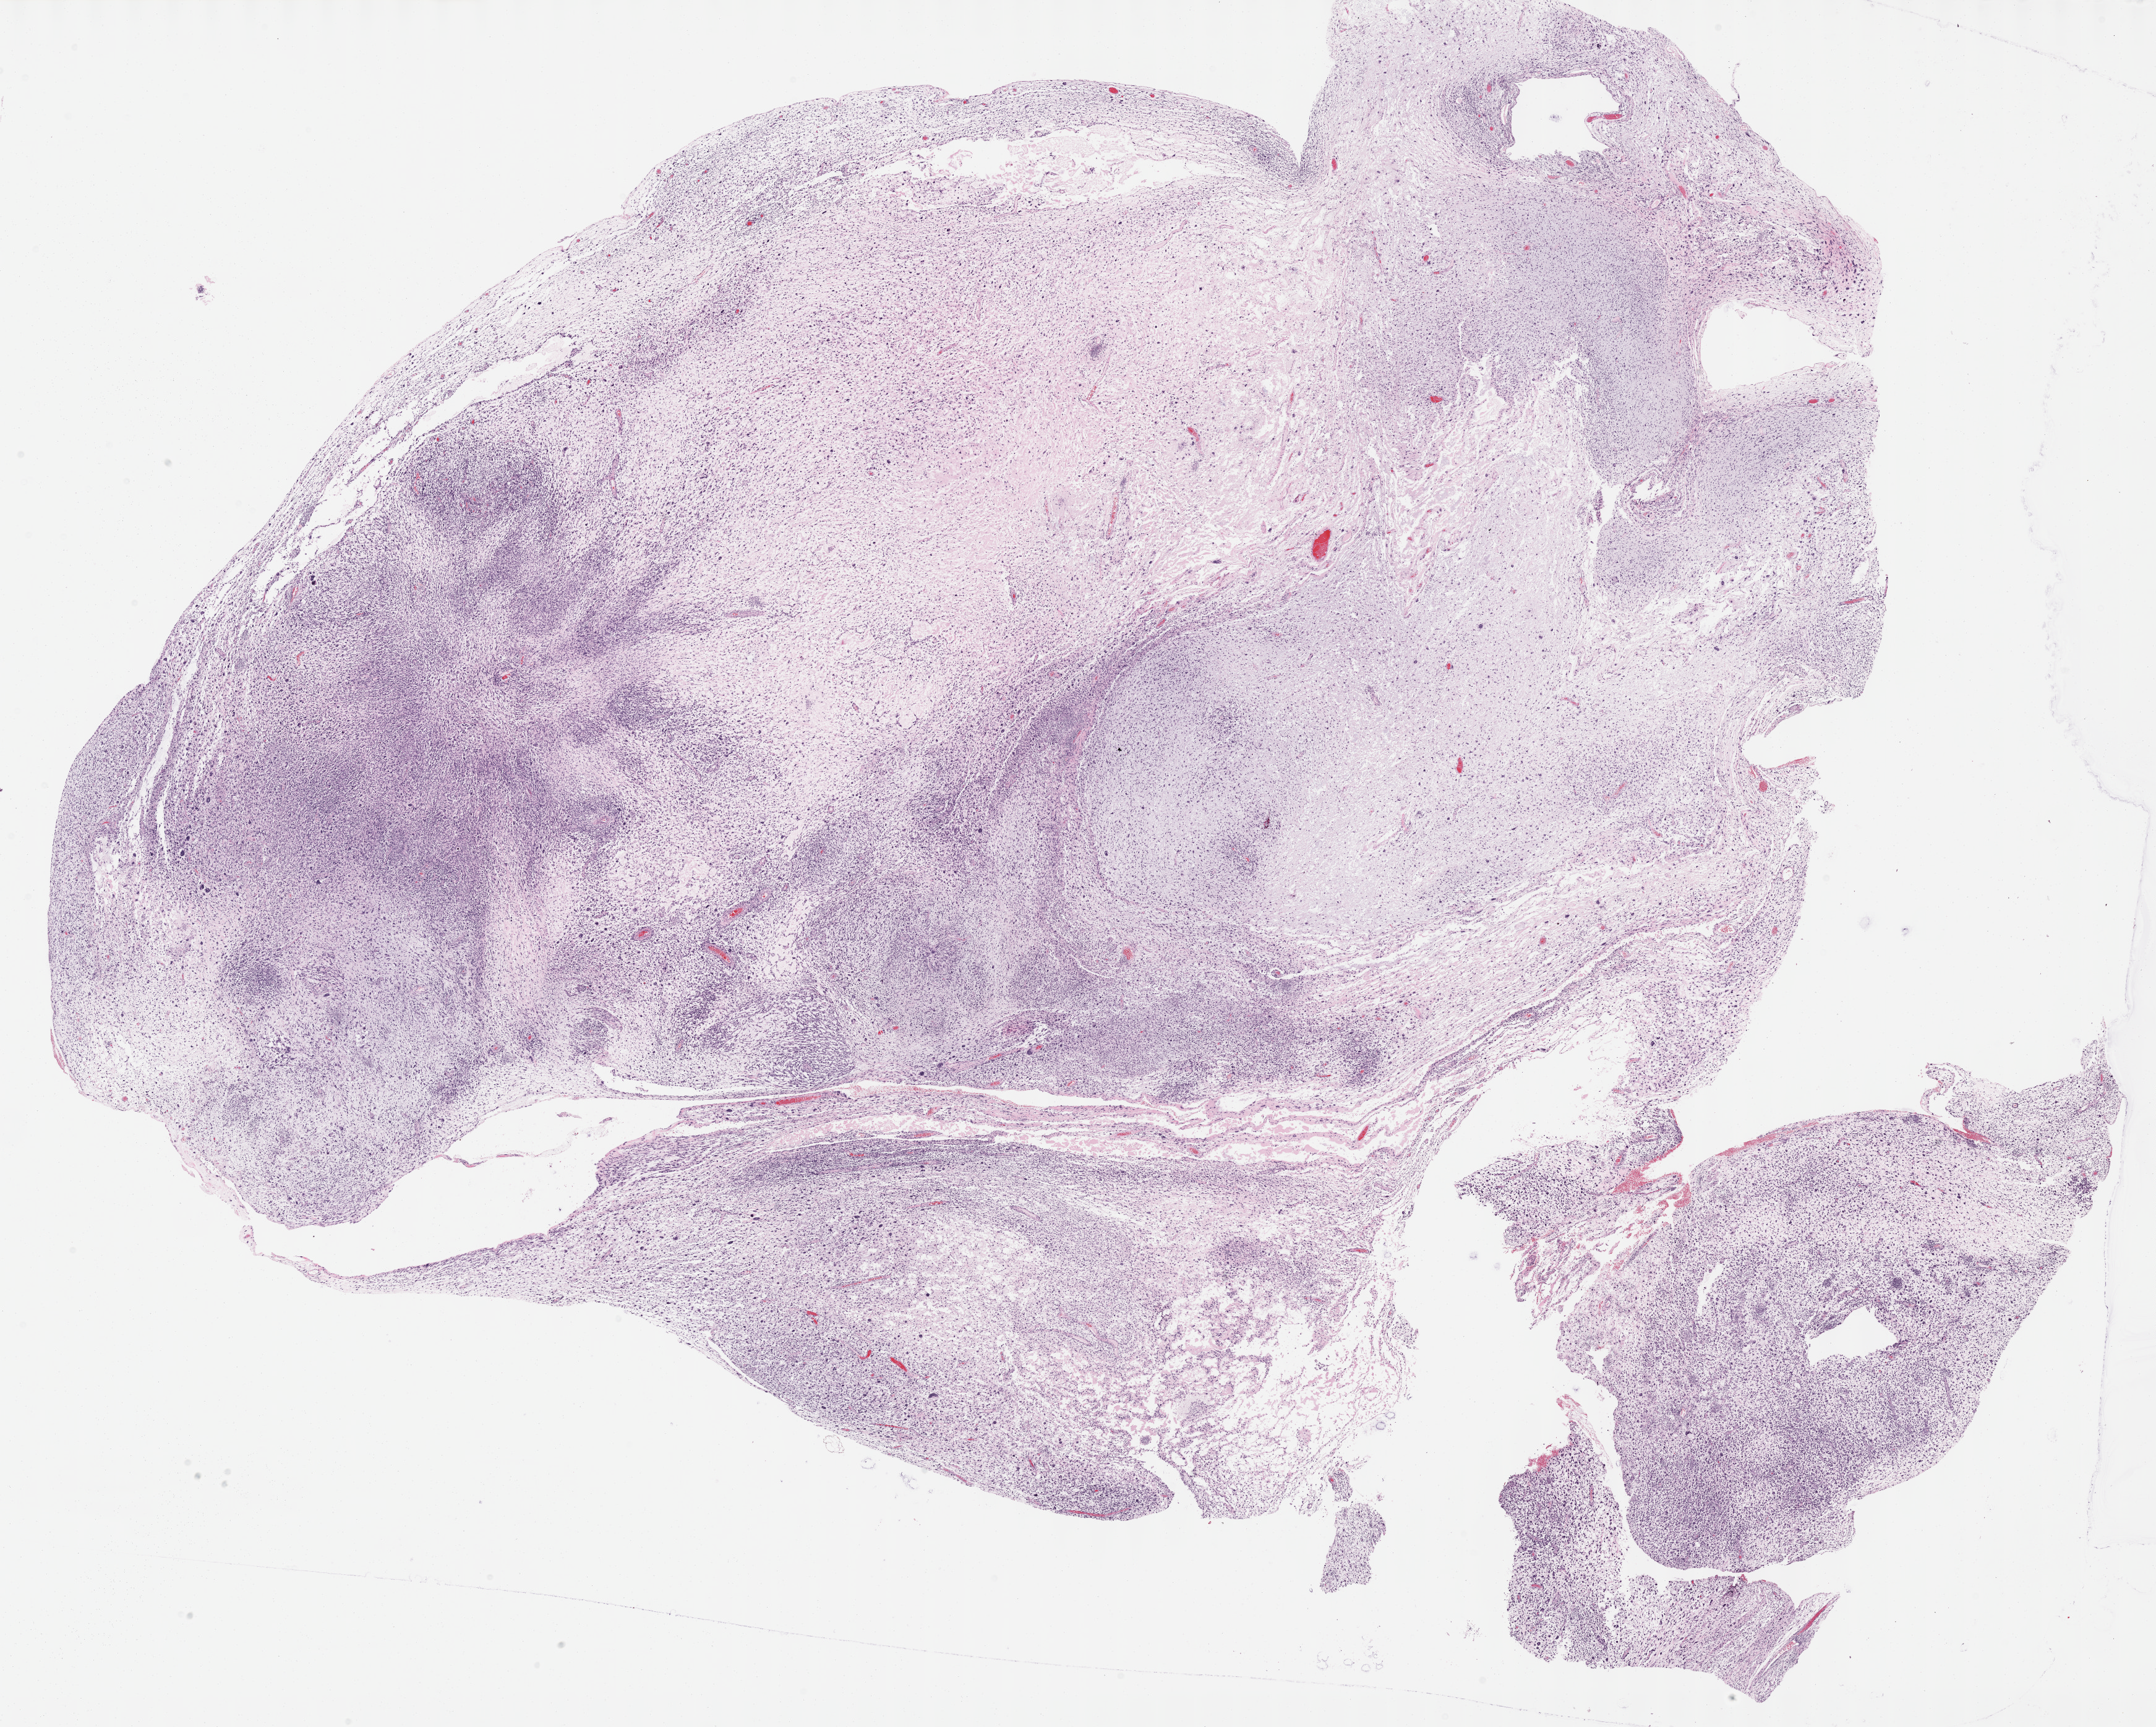
Digitized Hematoxylin and eosin (H&E) stained tissue section (whole slide) — shown as a low-resolution overview of the whole scanned area (about 28.2 x 22.6 mm), FFPE section, sample: primary tumour, connective, subcutaneous and other soft tissues. Patient: female, age at initial diagnosis 83 years.
Diagnosis: Fibromyxosarcoma.